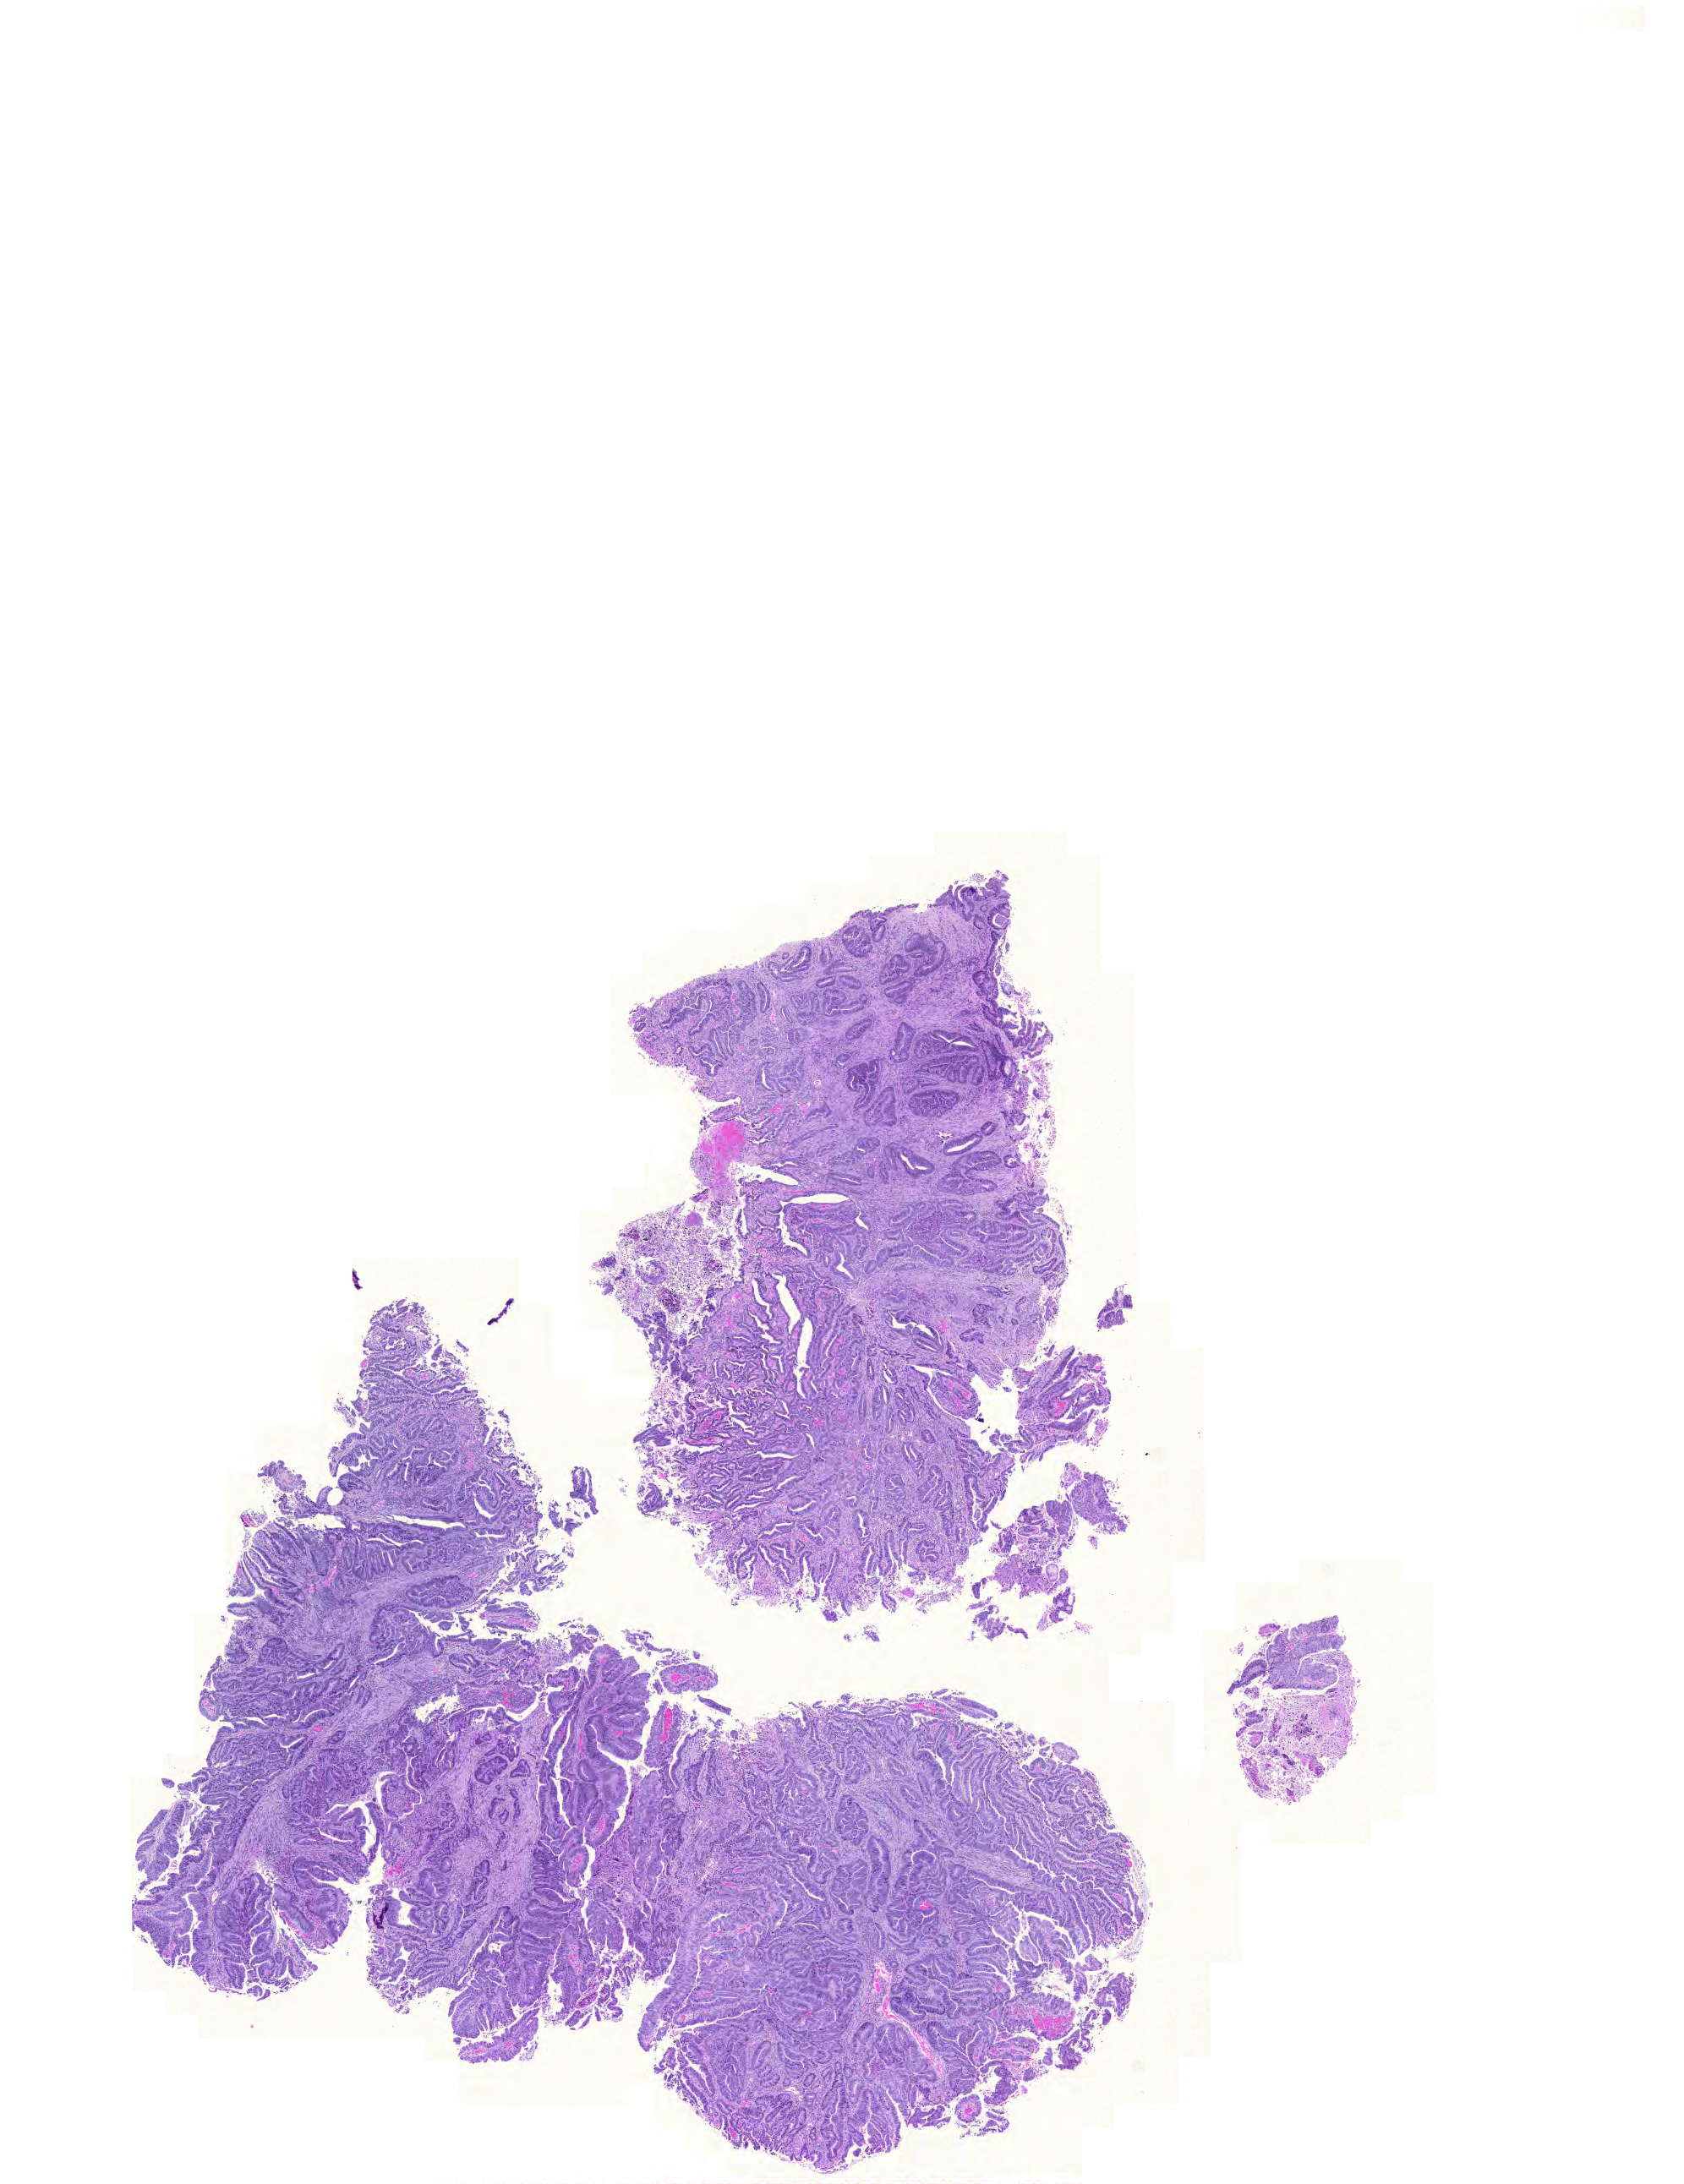
Hematoxylin and eosin (H&E) stained whole-slide image, a low-resolution overview of the entire scanned area, about 14.8 x 19.2 mm, formalin-fixed paraffin-embedded (FFPE) diagnostic section, rectum, primary tumour sample. Patient: female, age at initial diagnosis 55 years.
Diagnosis: Adenocarcinoma, NOS. Lymph nodes positive (case pathology): 1 of 32 examined. AJCC pathologic stage: IIIB (6th edition).